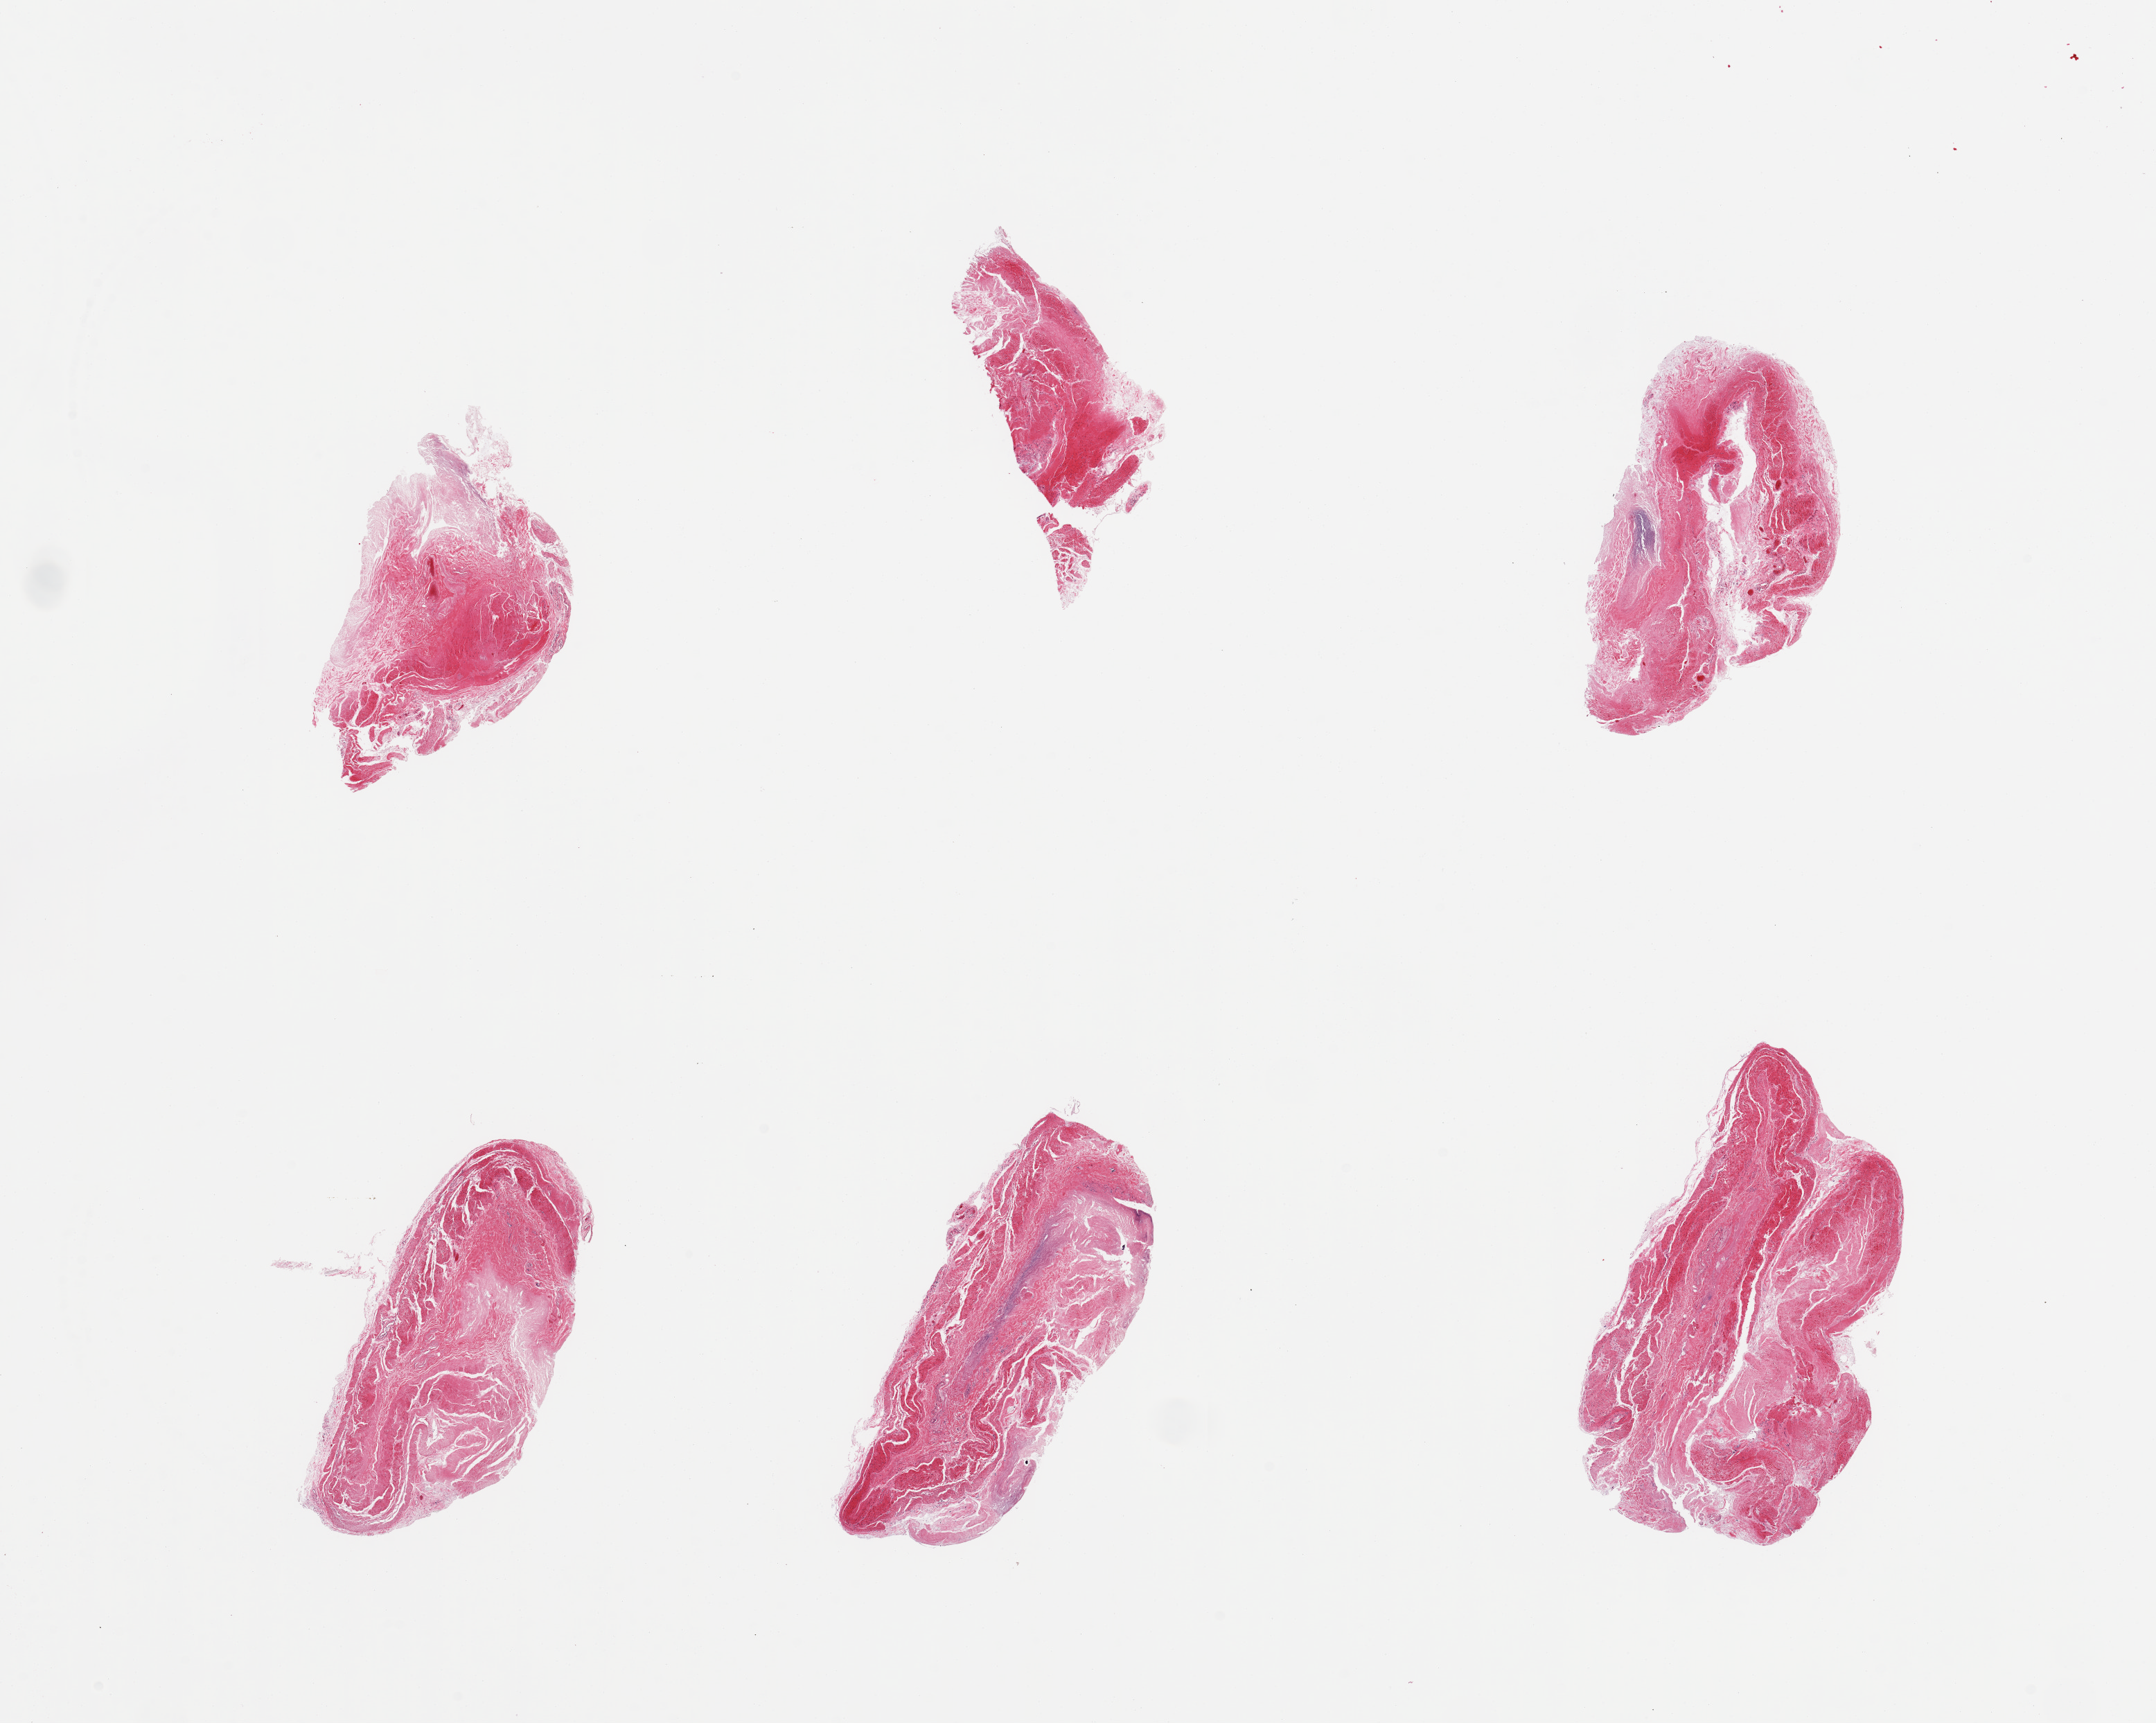
H&E whole-slide image, brightfield — shown as a low-resolution overview of the whole scanned area (about 24.6 x 19.7 mm, slide scanned at 20x). PAXgene-fixed, paraffin-embedded tissue. Sampled site (target tissue): ileum. Tissue donor sample. Donor: male.
Review note (as recorded): 6 pieces; severely autolyzed, no lymphoid nodules (target).